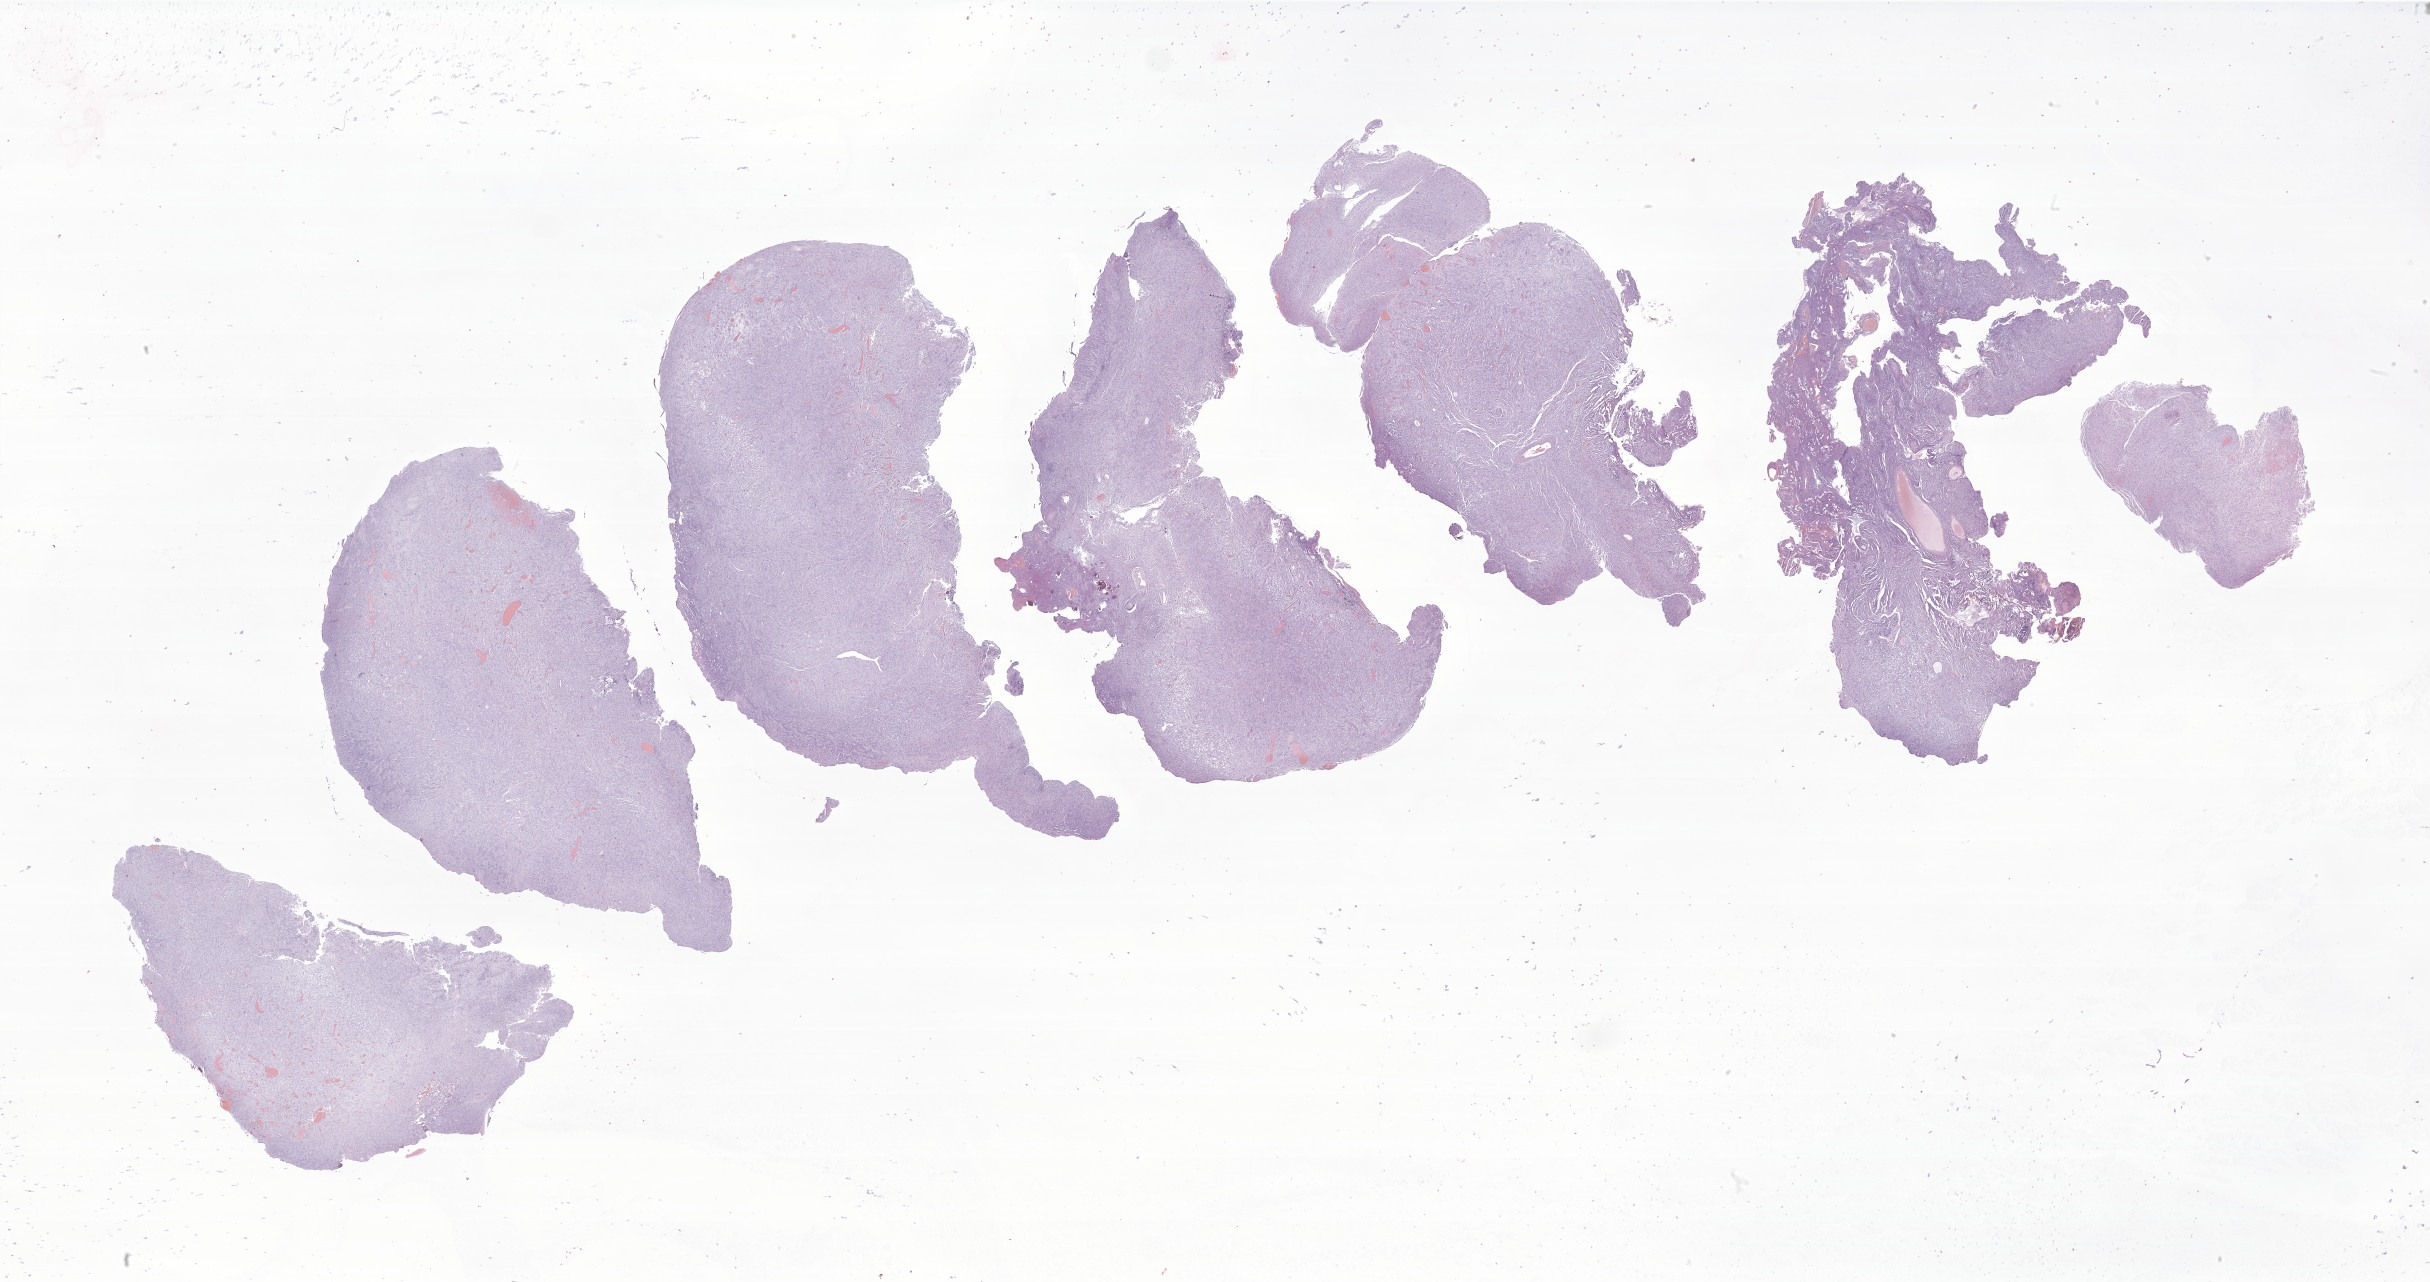
Digitized H&E-stained section of tumor tissue from the cerebral ventricle — shown as a low-resolution overview of the whole scanned area (about 41.0 x 21.6 mm); formalin-fixed, paraffin-embedded (FFPE) tissue. Female patient, age 109 months (9 years 1 month).
Diagnosis (ICD-O-3 morphology term): Glioma, malignant.